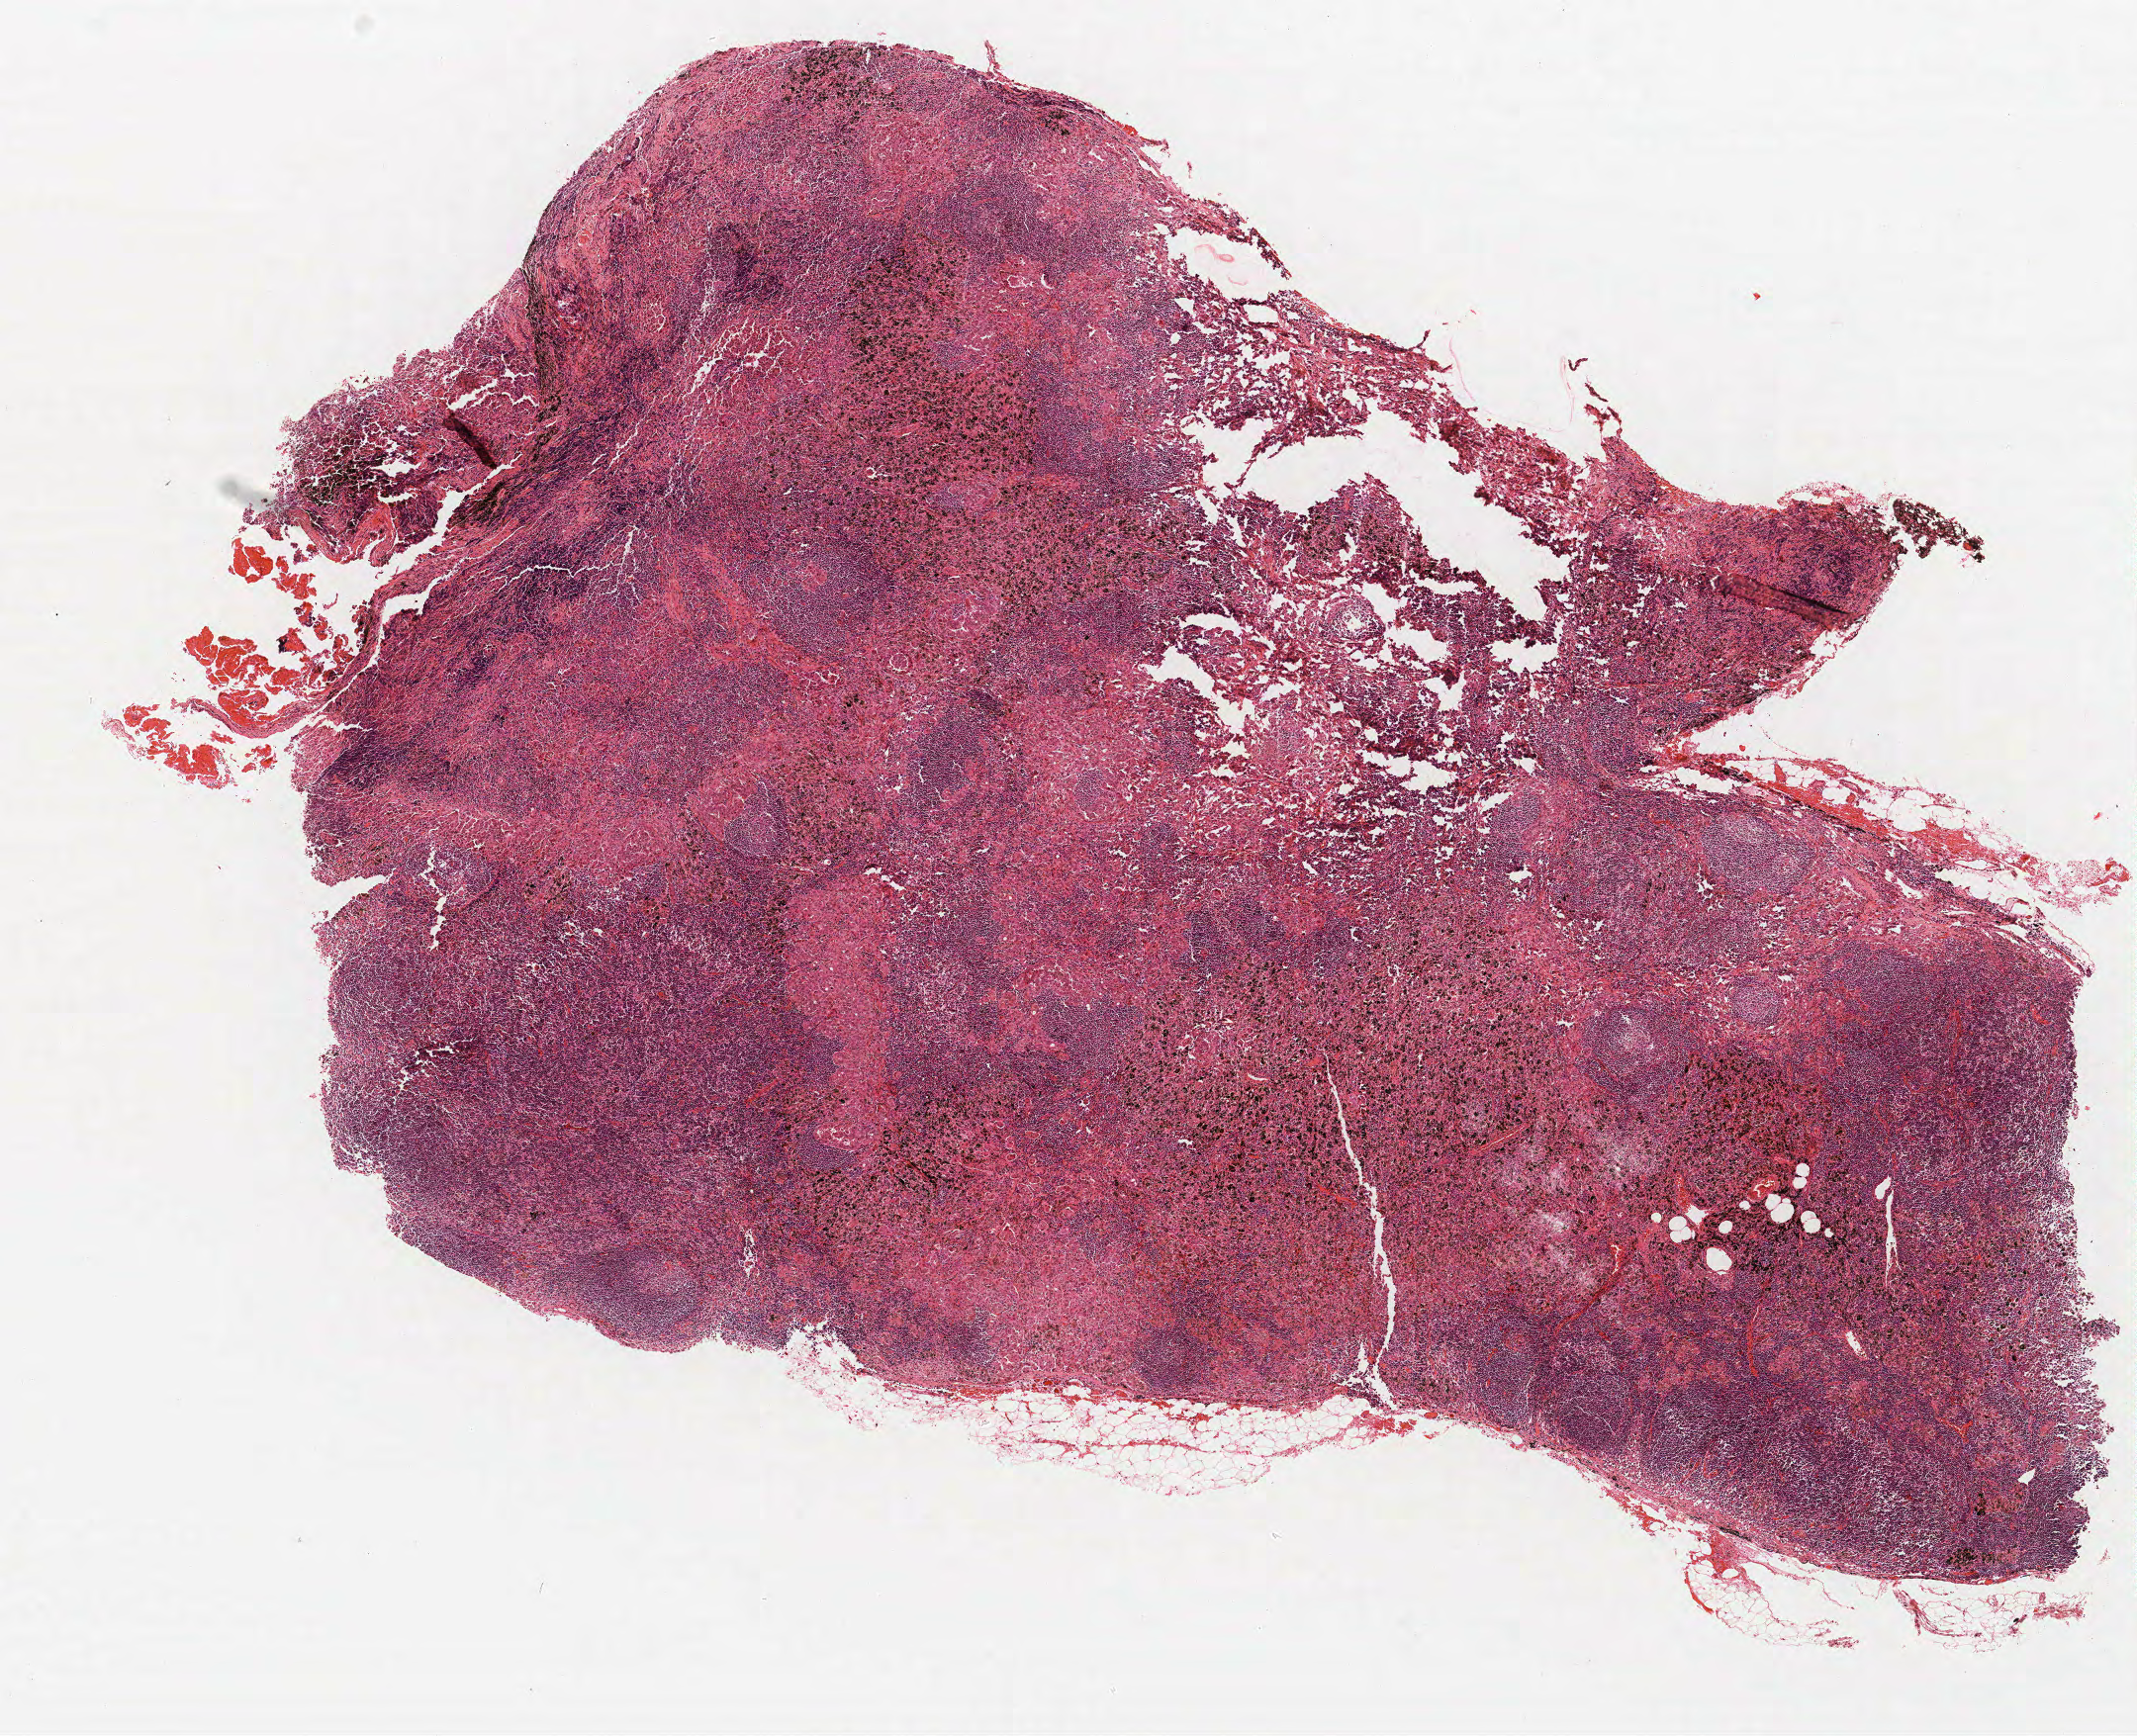
Whole-slide histology image, H&E, a low-resolution overview of the entire scanned area, about 8.6 x 7.0 mm (slide scanned at 40x). Formalin-fixed paraffin-embedded (FFPE) section. Lung. Female patient, aged 55 at enrolment. Grade: moderately differentiated (G2).
Participant's lung-cancer diagnosis: Bronchiolo-alveolar adenocarcinoma, NOS. Stage (AJCC 6th edition): IIA. ICD-O-3 topography: upper lobe of lung (C34.1). Primary tumour location (clinical record): right upper lobe. Tumour size (pathology): 13 mm.